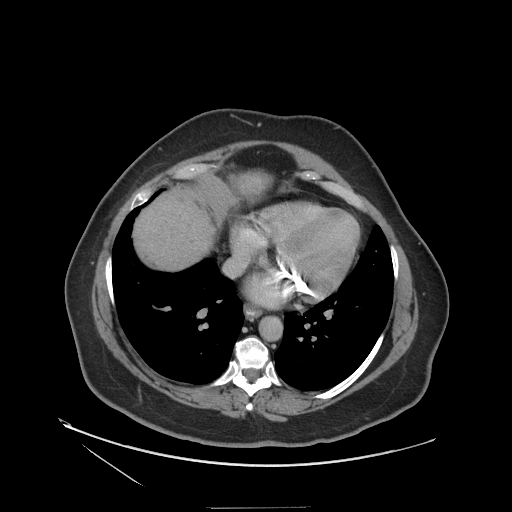
Contrast-enhanced abdominal CT (liver protocol), one axial slice; slice 108 of 127 in the series (ordered by position); 140 kVp; soft-tissue window (W 400 / L 40 HU); 512 × 512 image matrix, field of view 480 × 480 mm. From the clinical record (not read from this slice): diagnosis: hepatocellular carcinoma (patient treated with transarterial chemoembolisation; whether this scan precedes or follows treatment is not stated here); TNM stage (as recorded): Stage-II; Child-Pugh class: A; tumour differentiation: well differentiated; tumour nodularity: multinodular.
Structures marked on this image (semi-automatic segmentation, software-assisted and operator-edited):
- liver parenchyma outside the tumour (the mass and vessels are separate outlines, so this box may not span the whole liver): bounding box (x1, y1, x2, y2) in pixels: (134, 176, 262, 268)